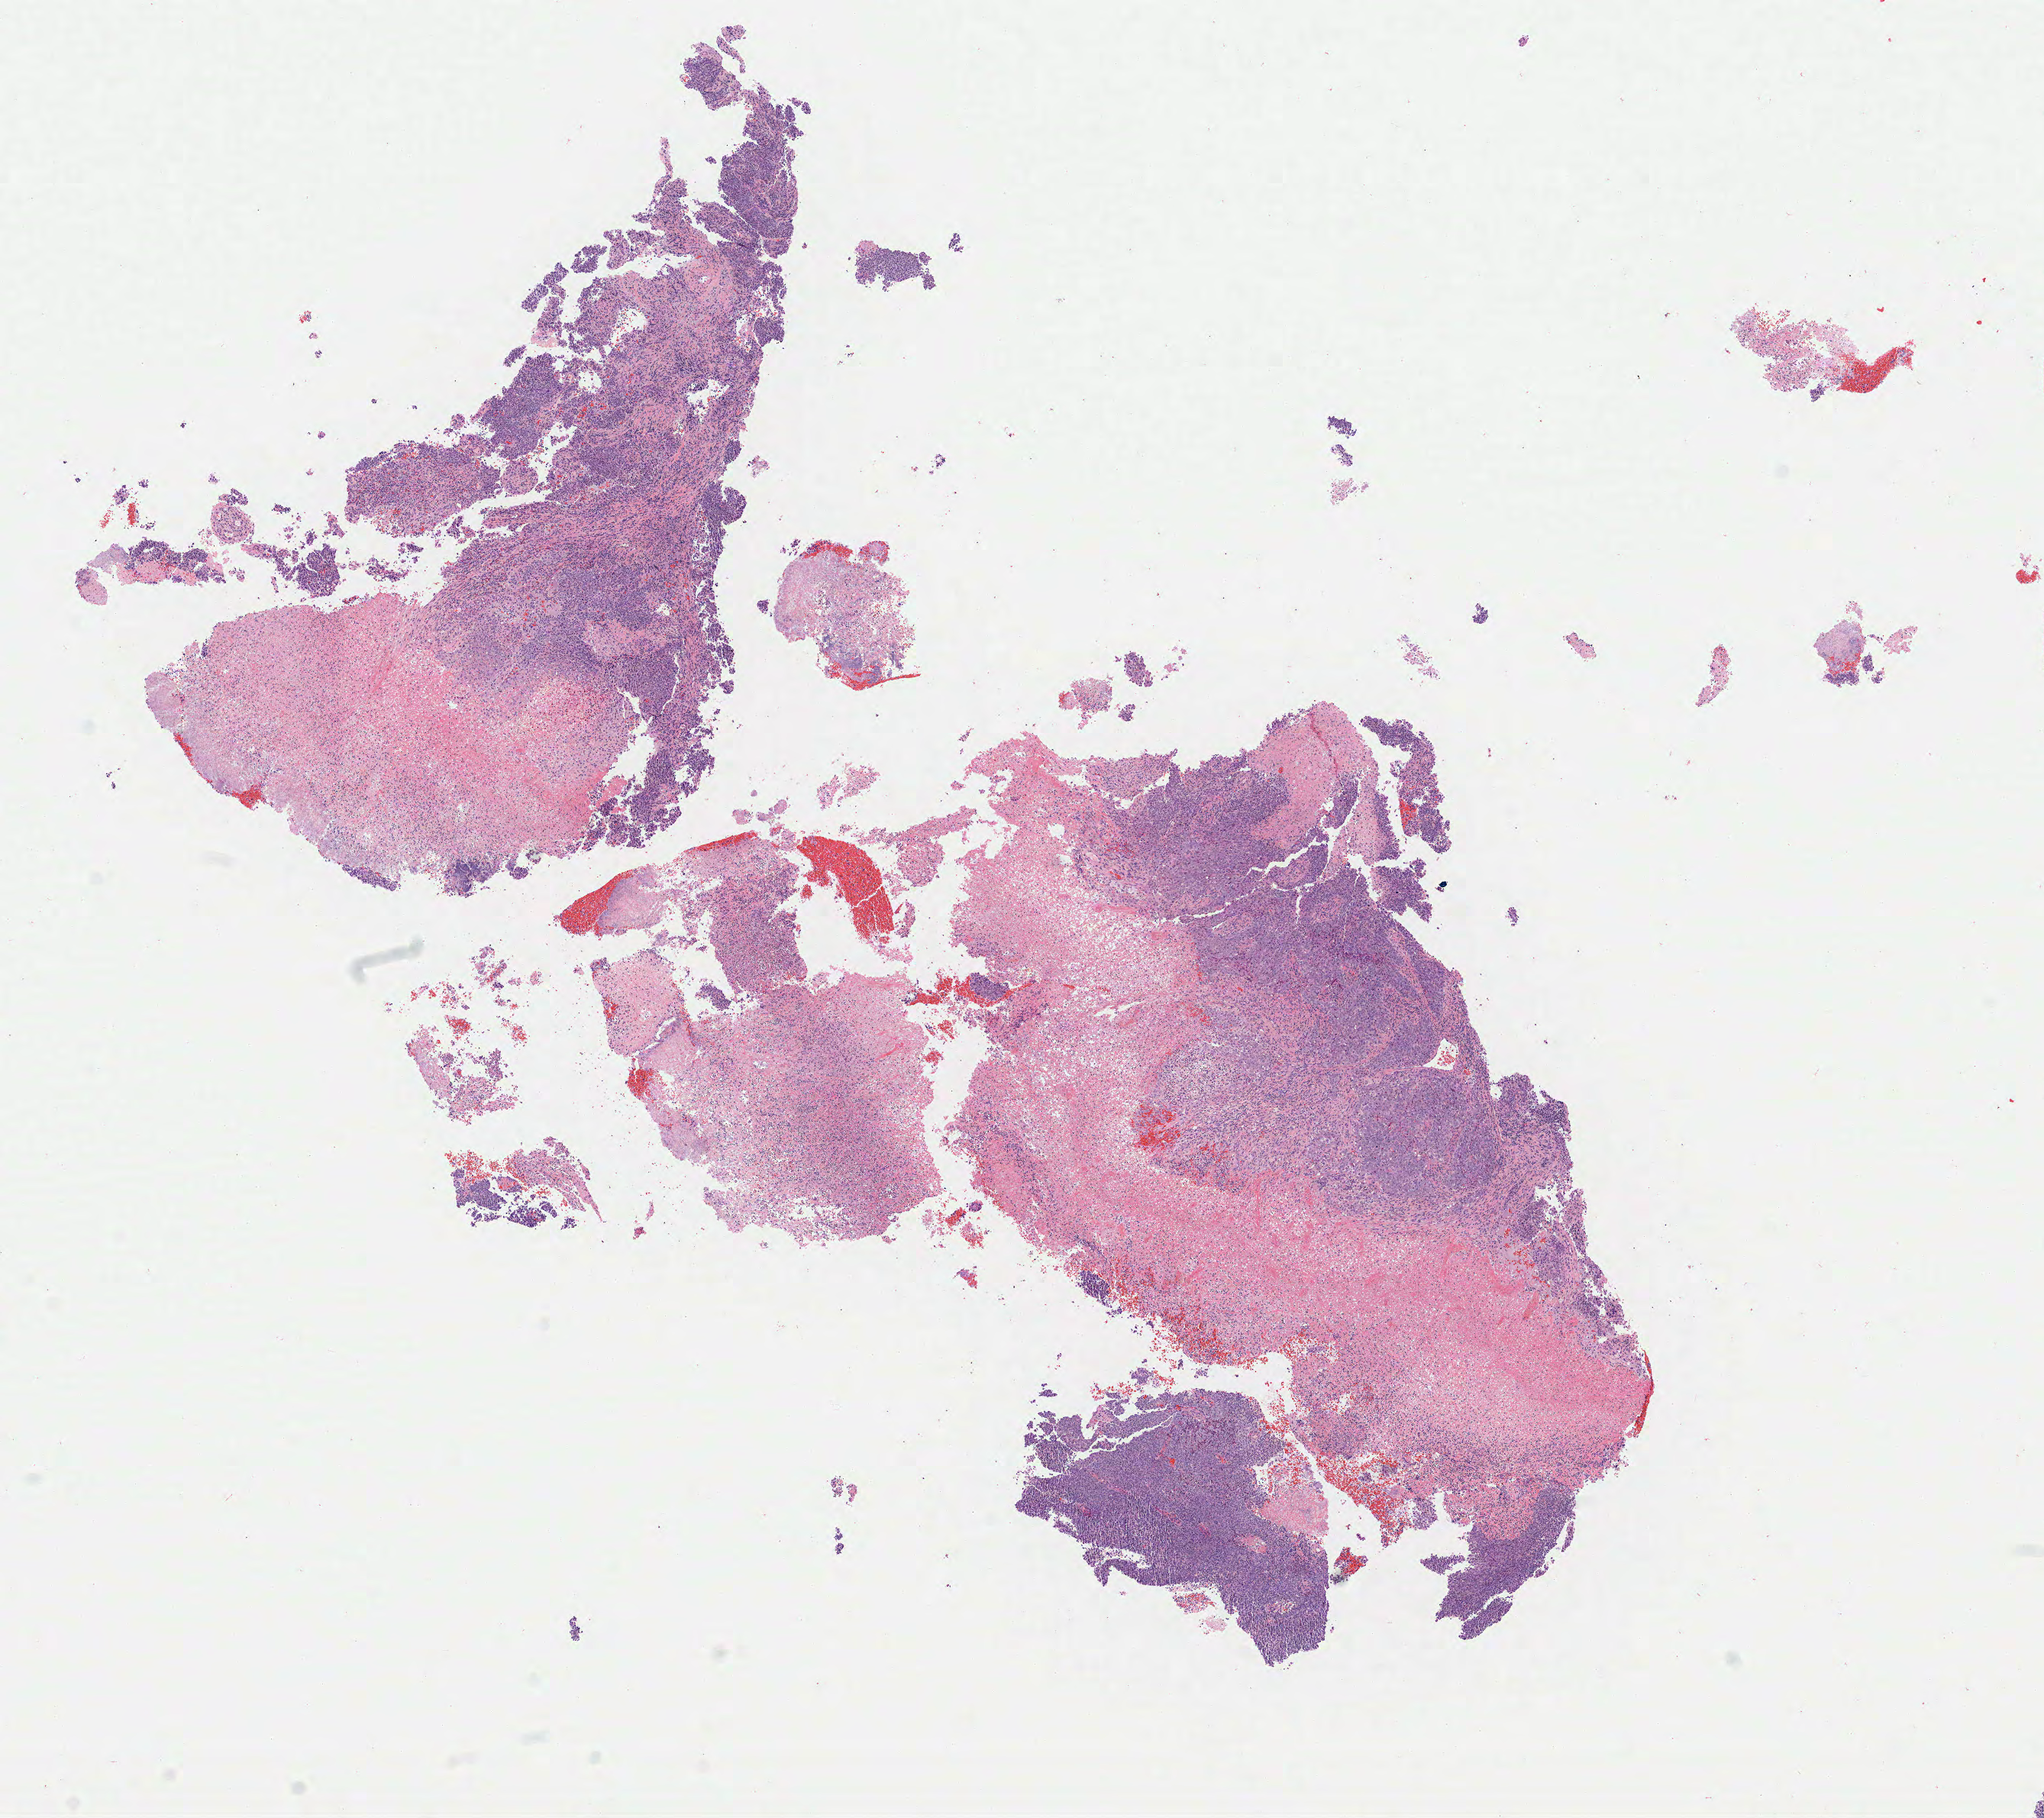
Digitized H&E-stained section, shown as a low-resolution overview of the whole scanned area (about 10.7 x 9.5 mm); tumor tissue; anatomic site: cervix. Female patient, 65 years old.
Diagnosis: Squamous cell carcinoma, large cell, nonkeratinizing, NOS.